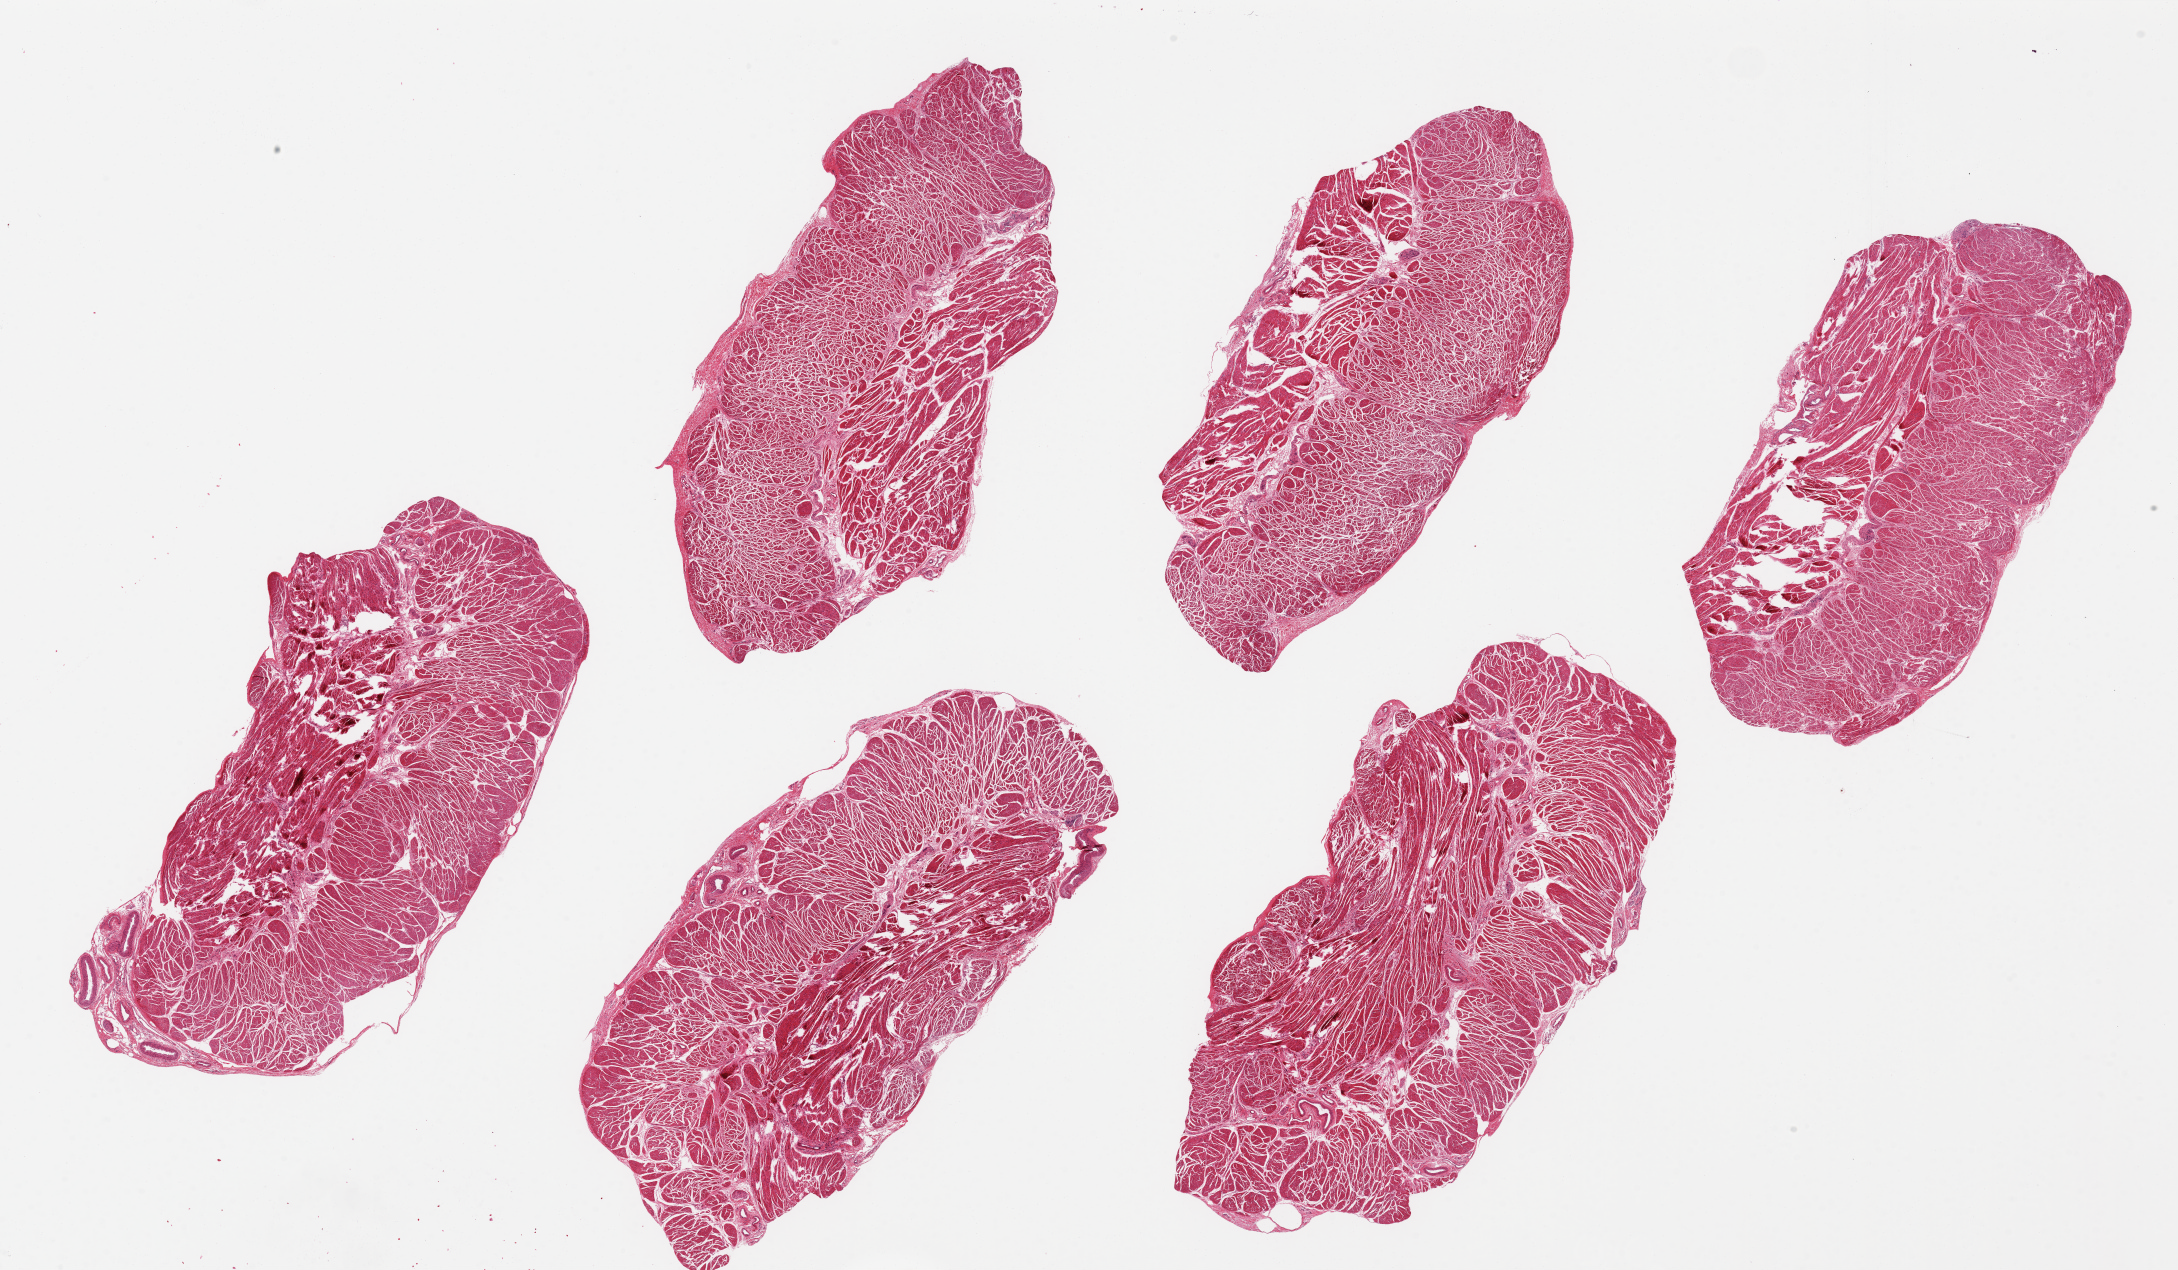
Digitized H&E-stained section, a low-resolution overview of the entire scanned area, about 34.5 x 20.1 mm. PAXgene-fixed, paraffin-embedded tissue. Target tissue: esophageal muscle. Tissue donor sample. Female donor.
* pathologist's review note for this sample: 6 pieces up to 10x4 mm; good muscle